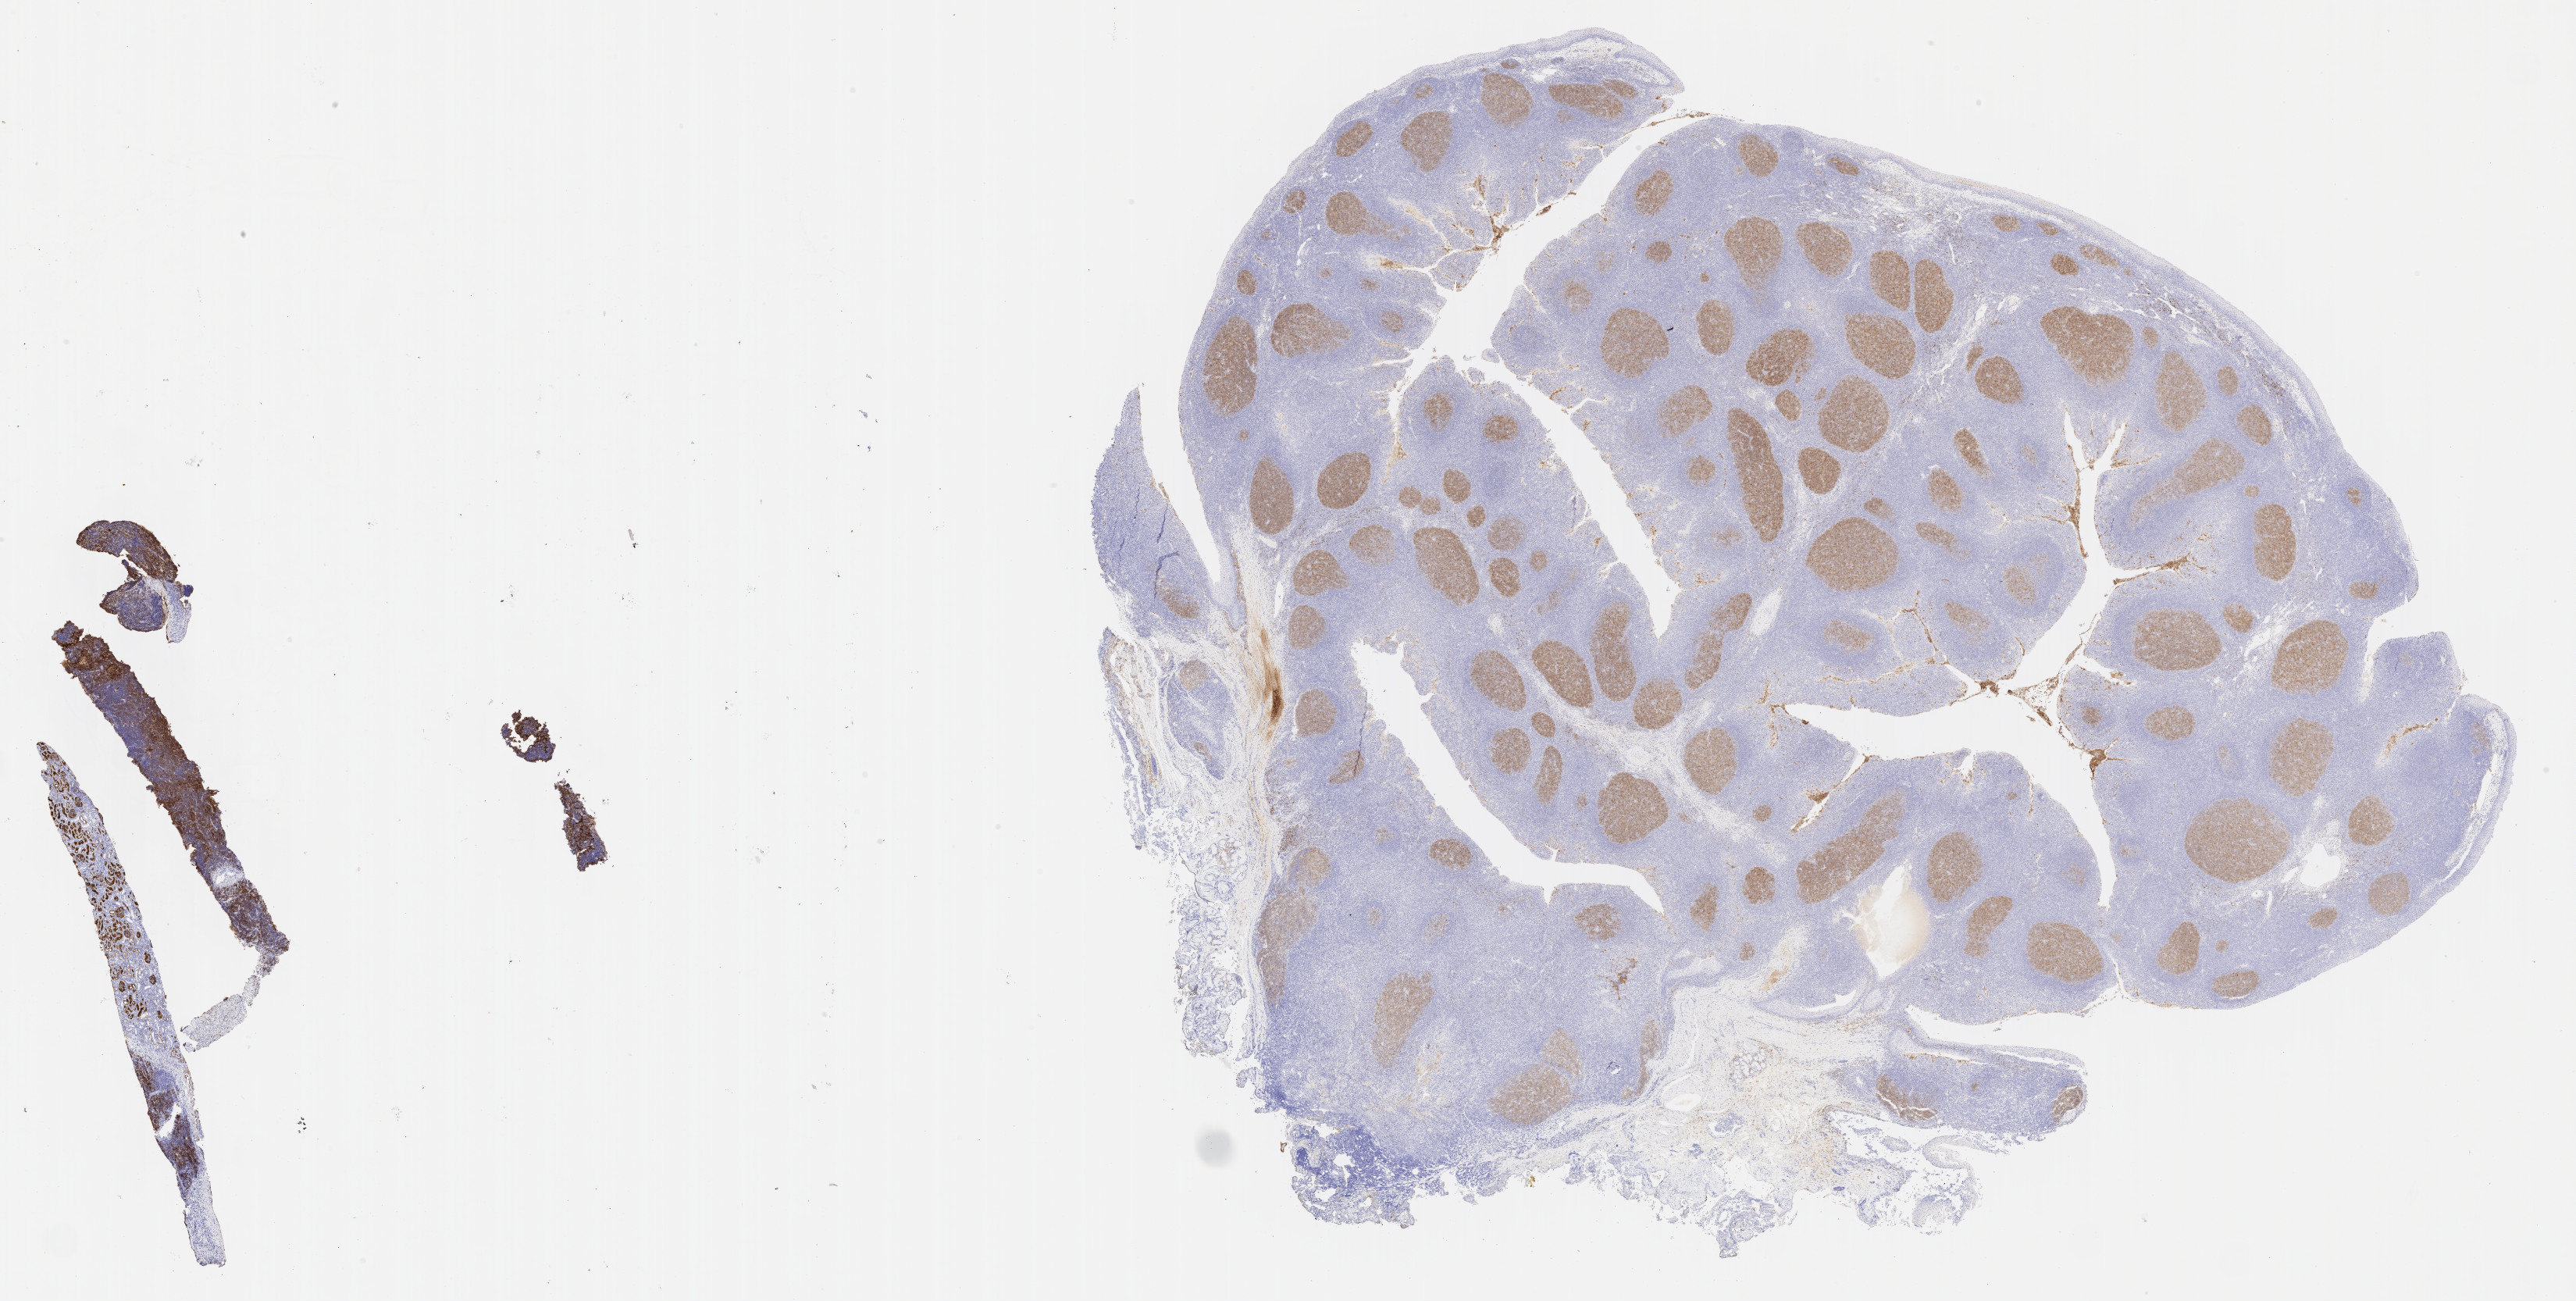
IHC for CD10, whole-slide image, low-resolution overview of the scanned area, about 26.7 x 13.5 mm; specimen: tumor tissue; anatomic site: liver. Male, age 8 years at initial diagnosis.
- histologic diagnosis: Burkitt lymphoma, NOS